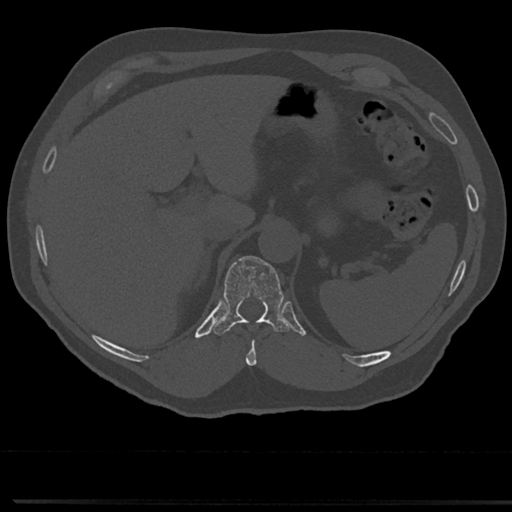
CT including the spine, one axial slice. Position 215 of 817 along the scan axis. Reconstruction kernel Br40s/3. Bone window (W 1800 / L 400 HU). 0.5 mm slice thickness. 512 × 512 image matrix, field of view 355 × 355 mm. Patient: male, 61 years. Case-level facts recorded for this patient, not image findings: primary cancer: prostate.
Annotated regions visible in this slice (semi-automatically segmented with operator editing):
- T10 vertebra: bounding box [x1, y1, x2, y2] px = [246, 327, 262, 366]
- T11 vertebra: [215, 256, 288, 335]